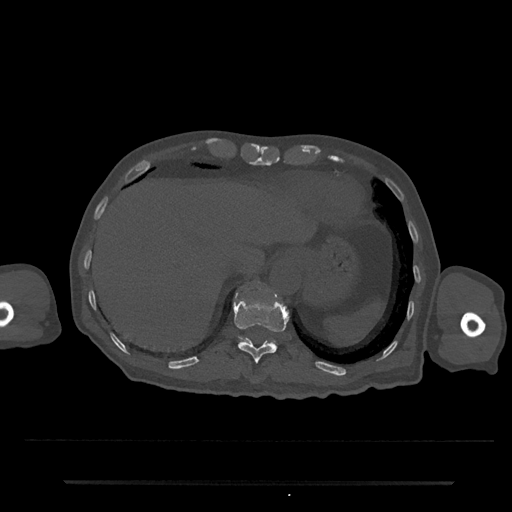
CT including the spine, one axial slice. Position 247 of 797 along the scan axis. Reconstruction kernel Br40s/3. 120 kVp. Bone window (W 1800 / L 400 HU). 0.5 mm slice thickness. 512 × 512 image matrix. Patient: male, 74 years. From the clinical record (not read from this slice): primary cancer: prostate.
Outlined on this slice (semi-automatically segmented with operator editing):
- T11 vertebra: box from (x=233, y=296) to (x=289, y=364) px
- T12 vertebra: (x=239, y=337)–(x=274, y=343)